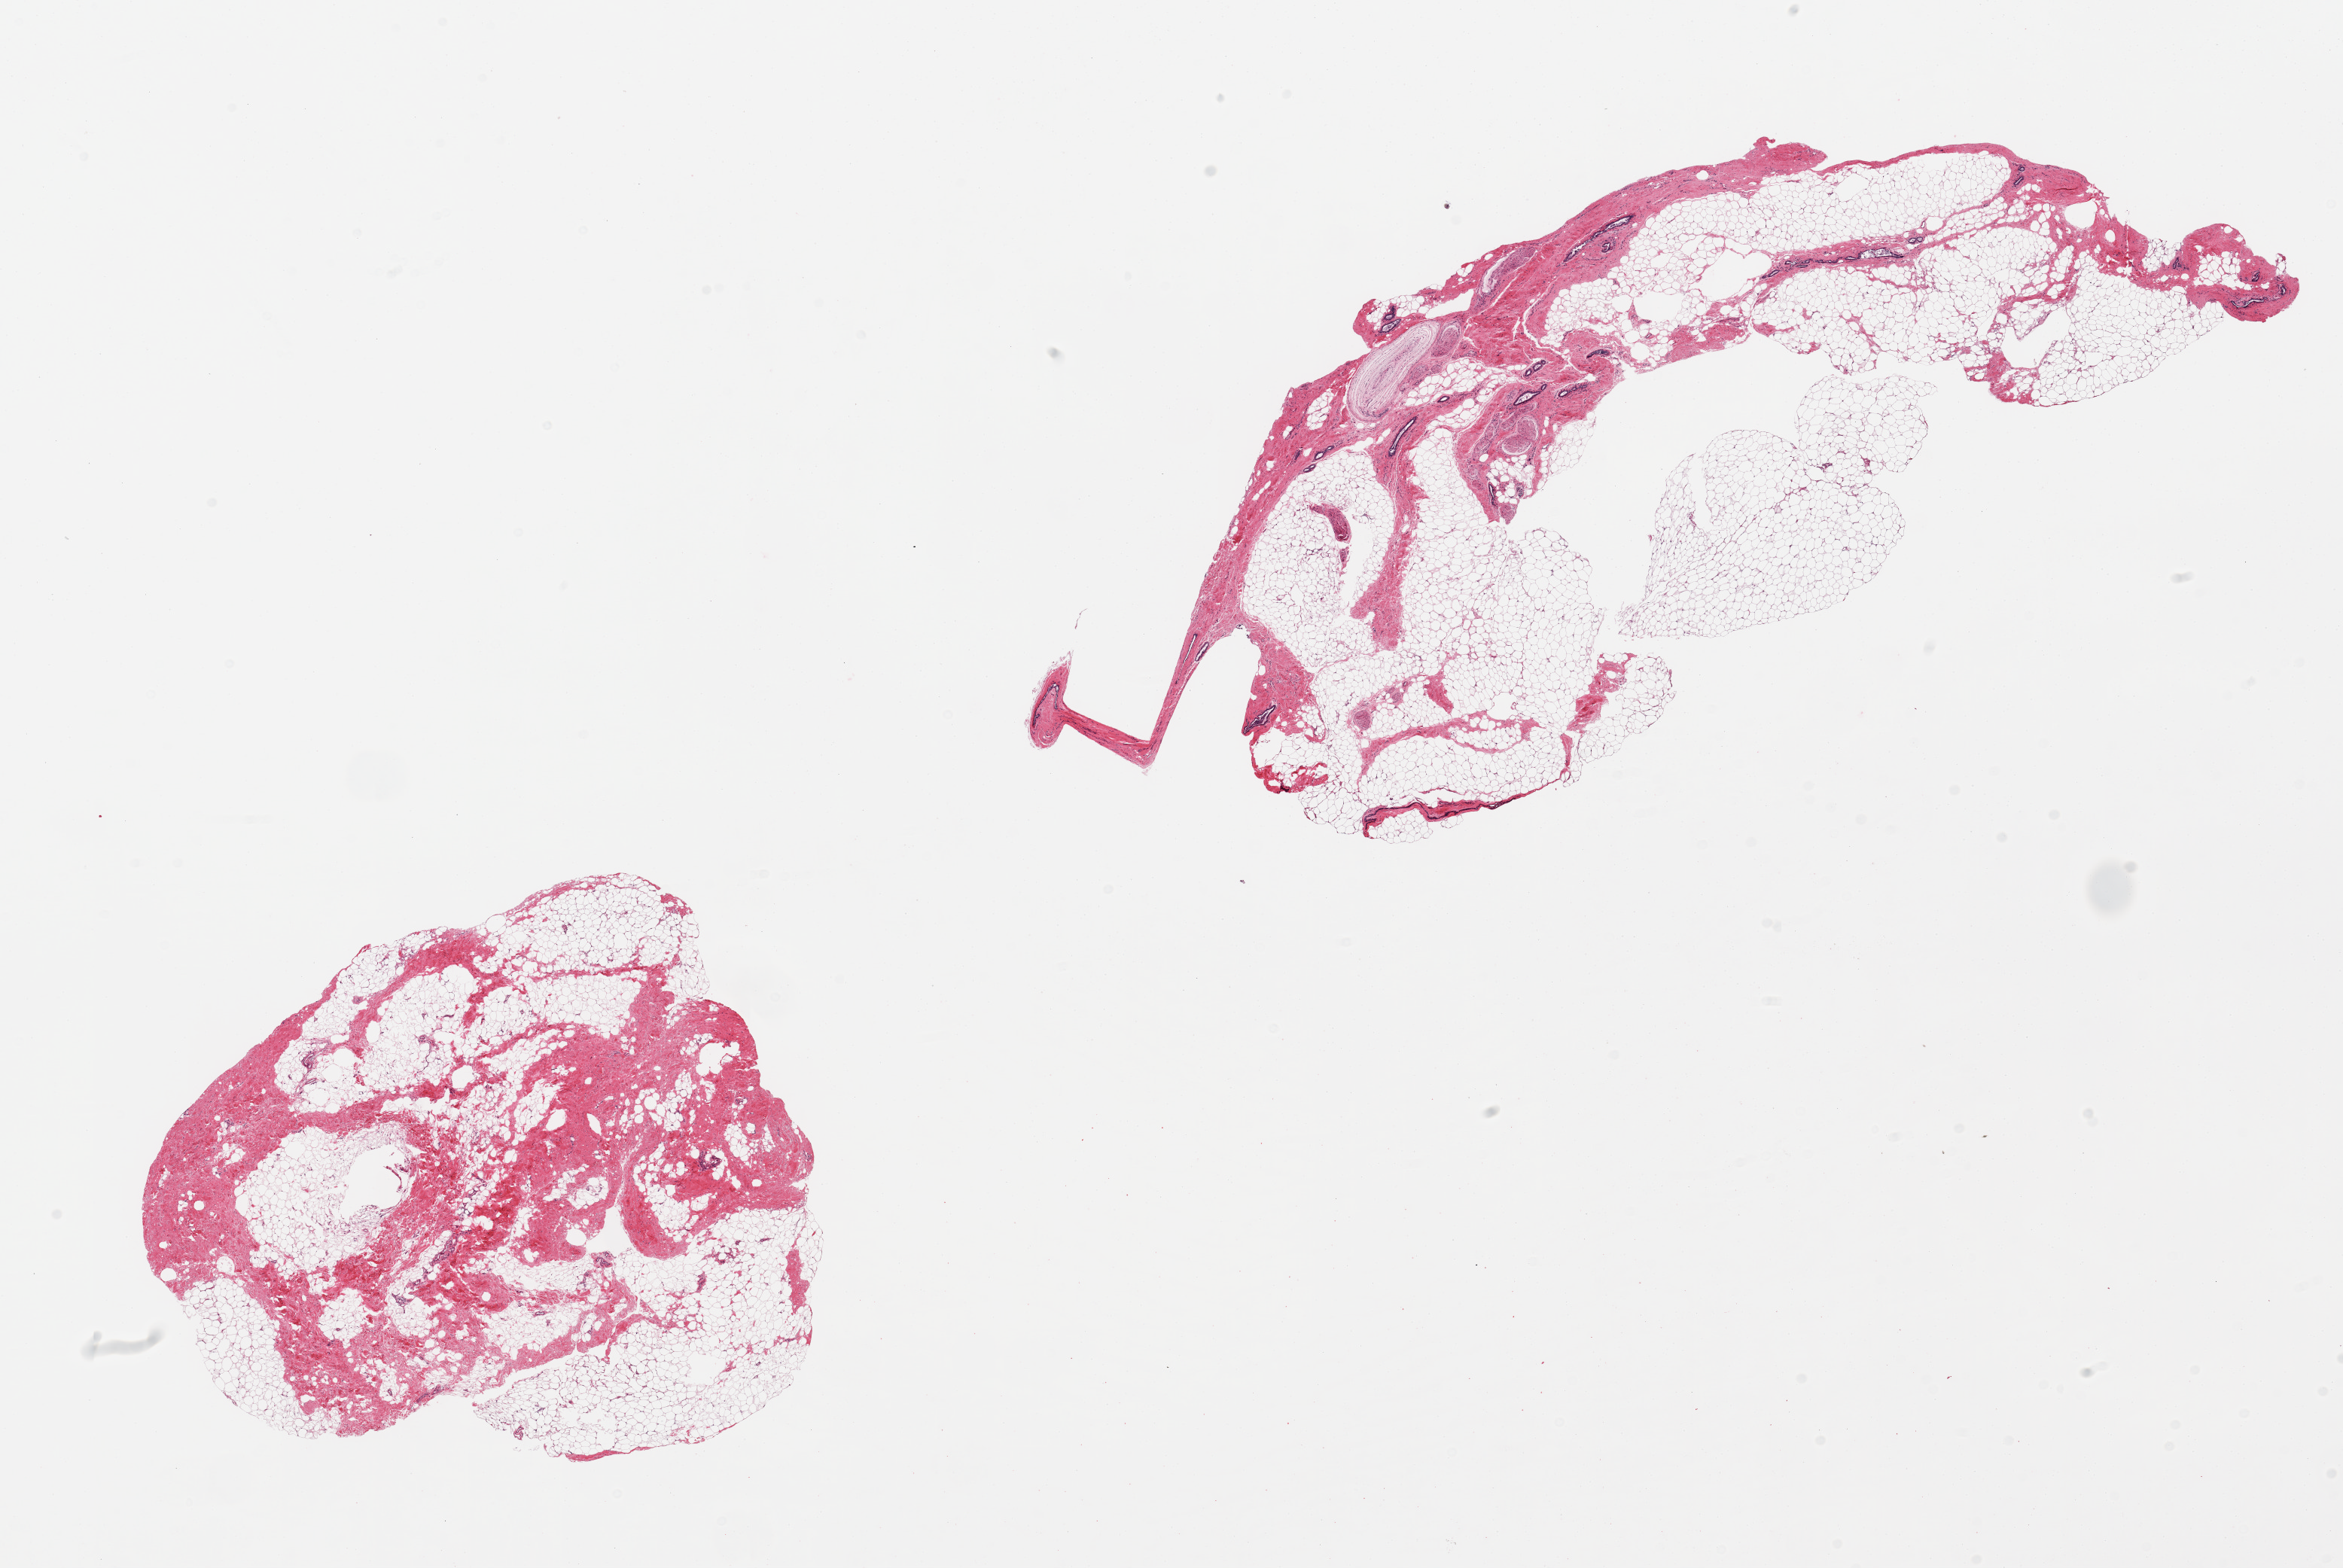
Digitized hematoxylin and eosin (H&E)-stained section — a low-resolution overview of the entire scanned area, about 24.6 x 16.5 mm (slide scanned at 20x). Donor: male.
• specimen: PAXgene-fixed paraffin-embedded (PFPE) section; section of breast (target tissue); donor tissue sample